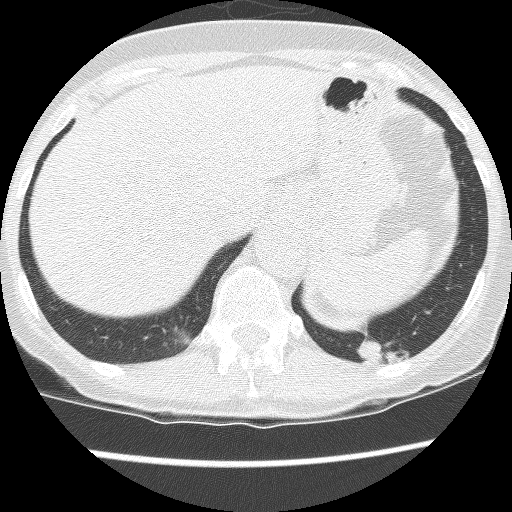
Axial slice from a low-dose chest CT screening exam. Third annual screen. Lung window (W 1500 / L -600 HU). Lung (sharp) reconstruction kernel (BONE). Slice 108 of 130 in the series. 512 × 512 image matrix. Female, age 61 years at enrolment. Current smoker at enrolment.
Expert reader's lesion annotation, bounding box [x1, y1, x2, y2] px = [337, 296, 438, 384]. The screening reader recorded 2 non-calcified nodules or masses ≥4 mm on this exam (left lower lobe, left lower lobe); which of them this box marks is not recorded. Lung cancer was diagnosed 166 days after this screen: non-small cell carcinoma, left lower lobe, poorly differentiated (G3), stage IB (AJCC 6th edition), 100 mm at pathology.